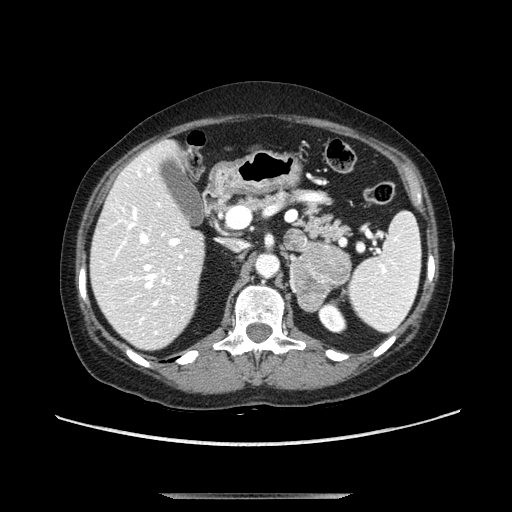
Contrast-enhanced abdominal CT, one axial slice. Slice 63 of 107 in the series (ordered by position). Soft-tissue window (W 400 / L 40 HU). 512 × 512 image matrix, field of view 380 × 380 mm. Female patient. Case-level facts recorded for this patient, not image findings: diagnosis: adrenocortical carcinoma; tumour side: left adrenal; tumour size at pathology: 7.5 cm; Ki-67 index: 9 %; stage (as recorded): 3.
Outlined on this slice (semi-automatic segmentation, software-assisted and operator-edited):
- mass: bounding box (x1, y1, x2, y2) in pixels: (291, 243, 352, 312)